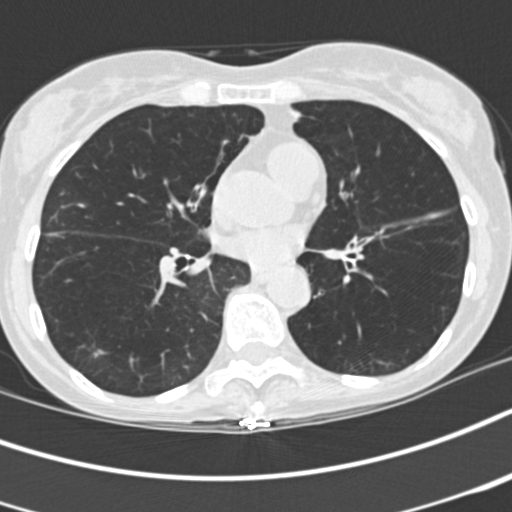
Low-dose screening chest CT, axial slice, baseline screening round, lung window (W 1500 / L -600 HU), standard (soft-tissue) reconstruction kernel (B30f), slice 99 of 197 in the series. Female, age 68 years at enrolment.
• Expert reader's lesion annotation, bounding box <76,340,115,369> (left, top, right, bottom; pixels).
• Reader record for this screening exam (exam-level; its link to the box is not recorded): non-calcified nodule or mass ≥4 mm, right lower lobe, 8 × 4 mm, spiculated (stellate) margins, soft tissue attenuation.
• Official screen result: positive, change unspecified: nodule(s) >= 4 mm or enlarging nodule(s), mass(es), or other non-specific abnormalities suspicious for lung cancer.
• Later outcome: lung cancer diagnosed 1012 days after this screen — squamous cell carcinoma, NOS, right lower lobe, stage IA (AJCC 6th edition).